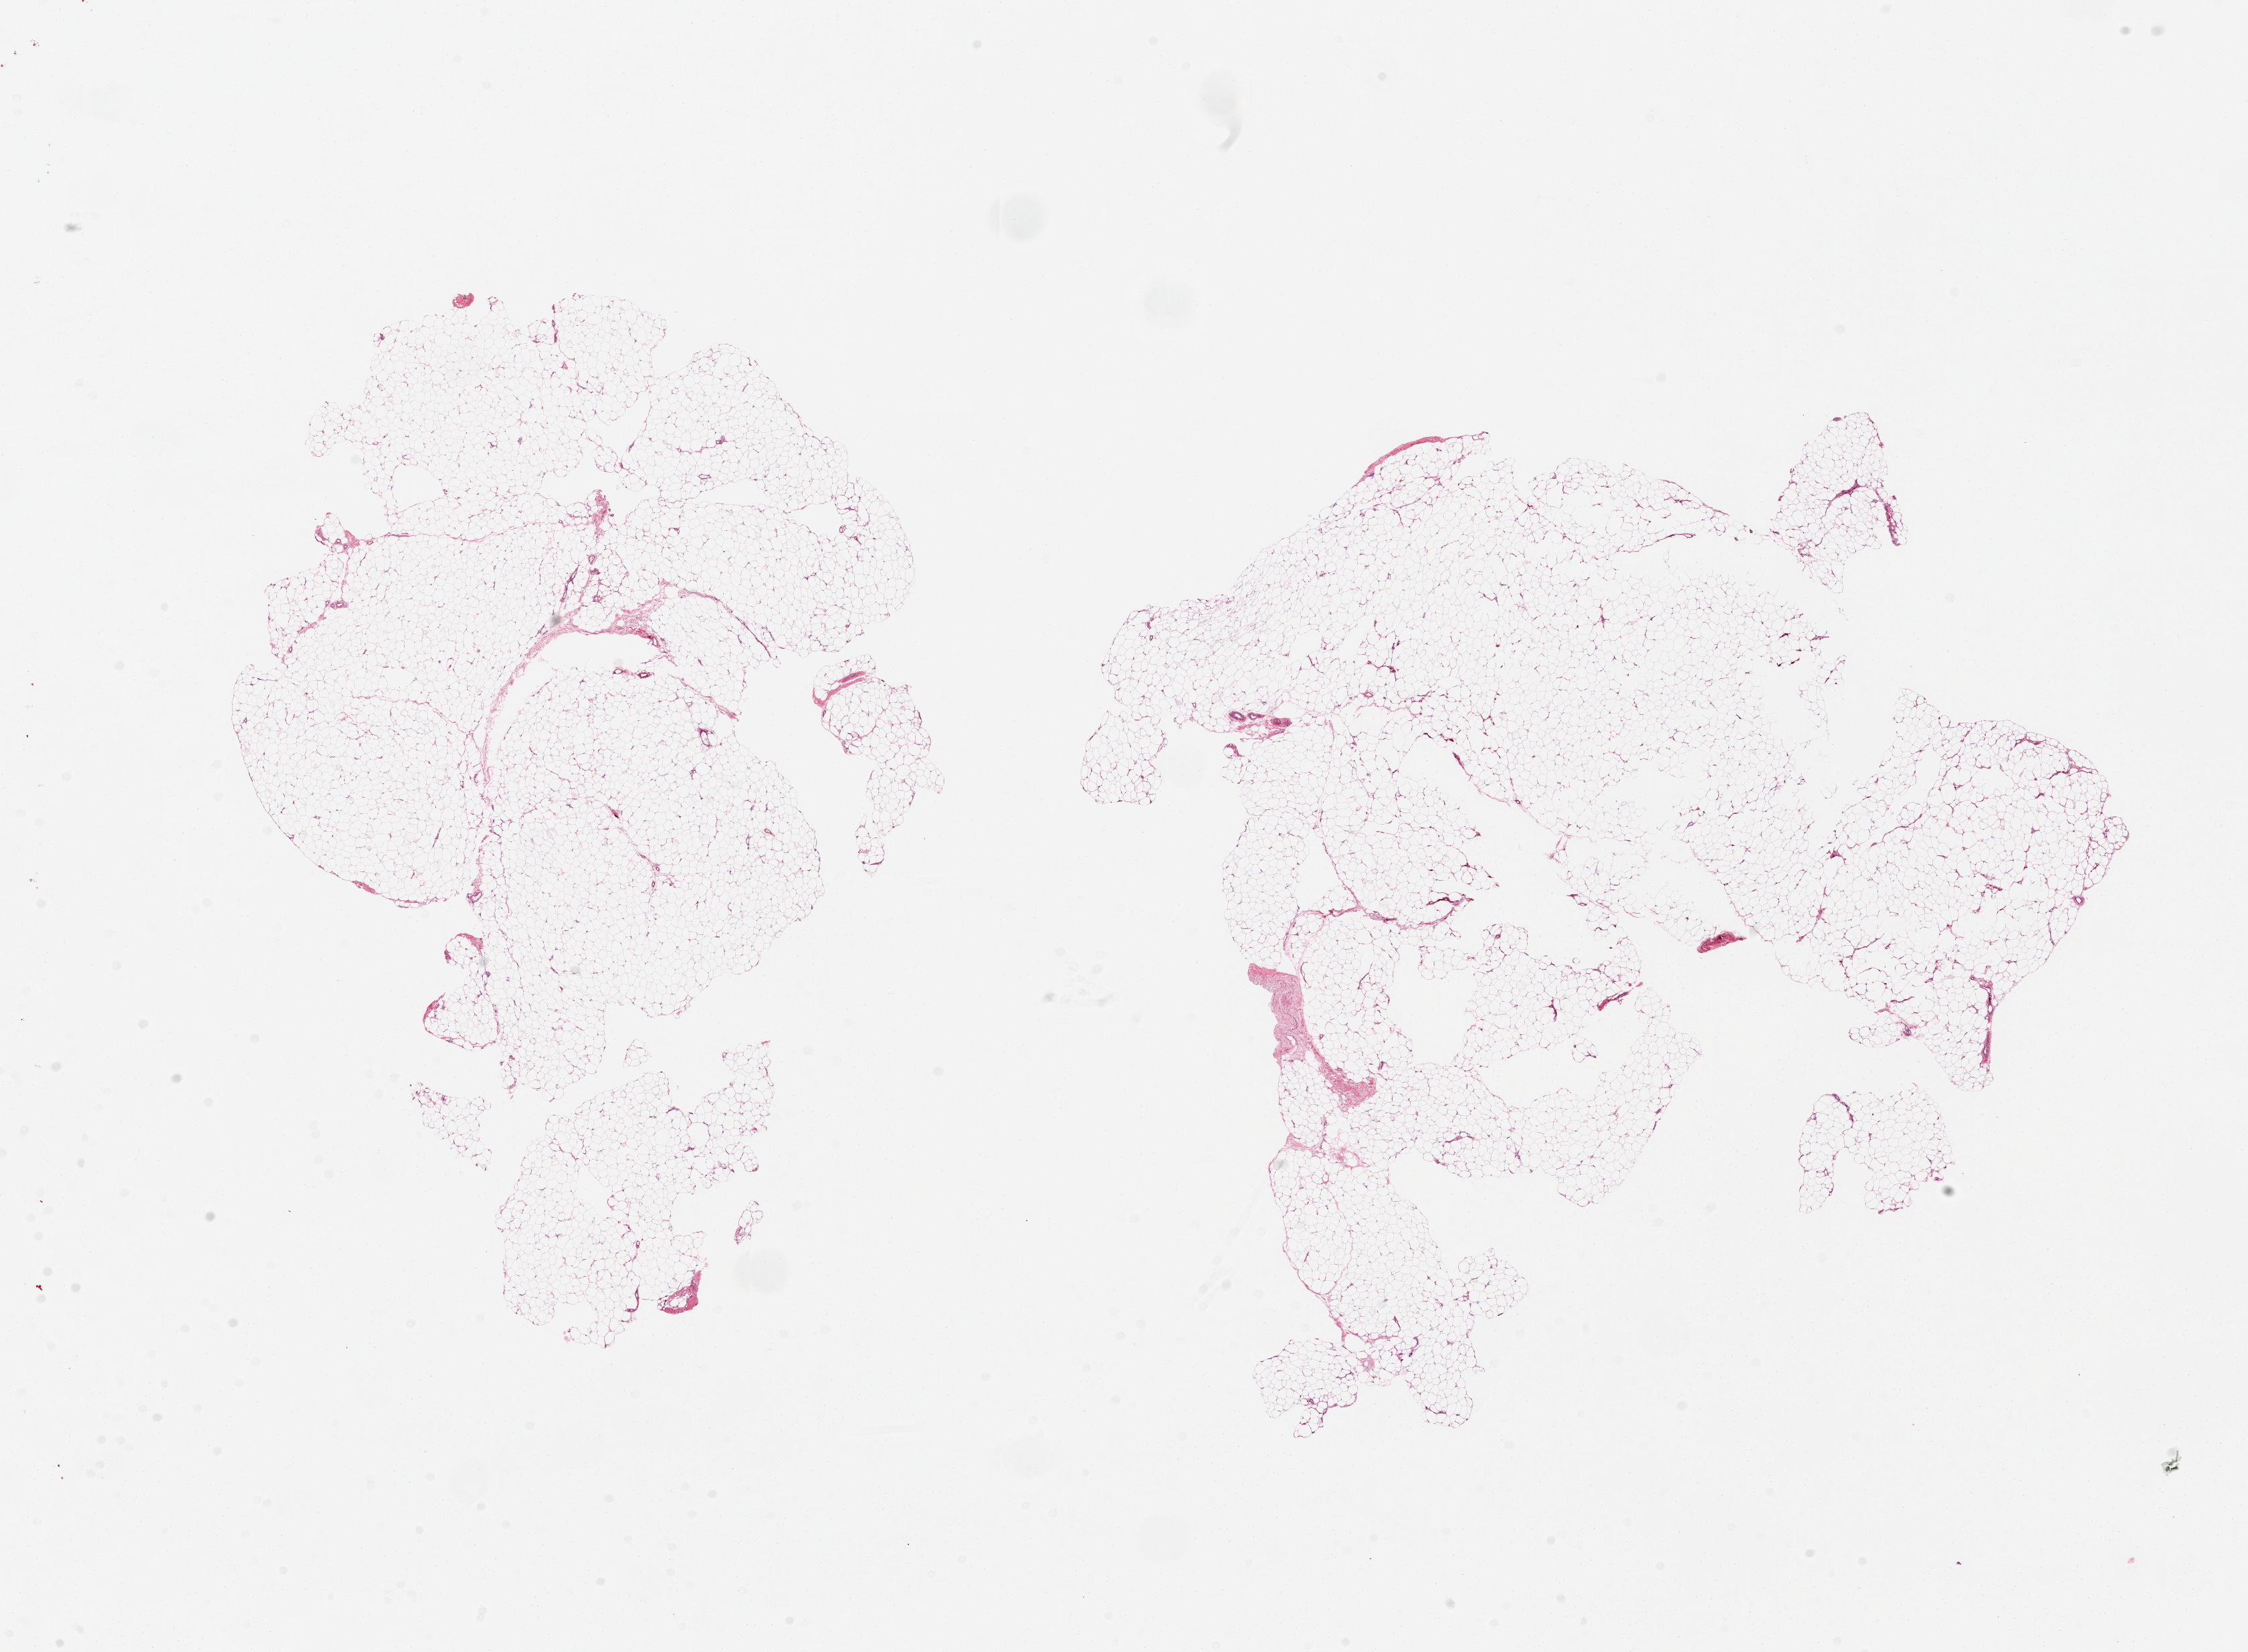
Whole-slide image, hematoxylin and eosin (H&E) stain, low-resolution overview of the scanned area, about 26.6 x 19.5 mm (from a 20x scan). PAXgene-fixed, paraffin-embedded tissue. Section of adipose tissue (target tissue). Donor tissue sample. Donor: female.
• pathologist's review note for this sample: 2 pieces